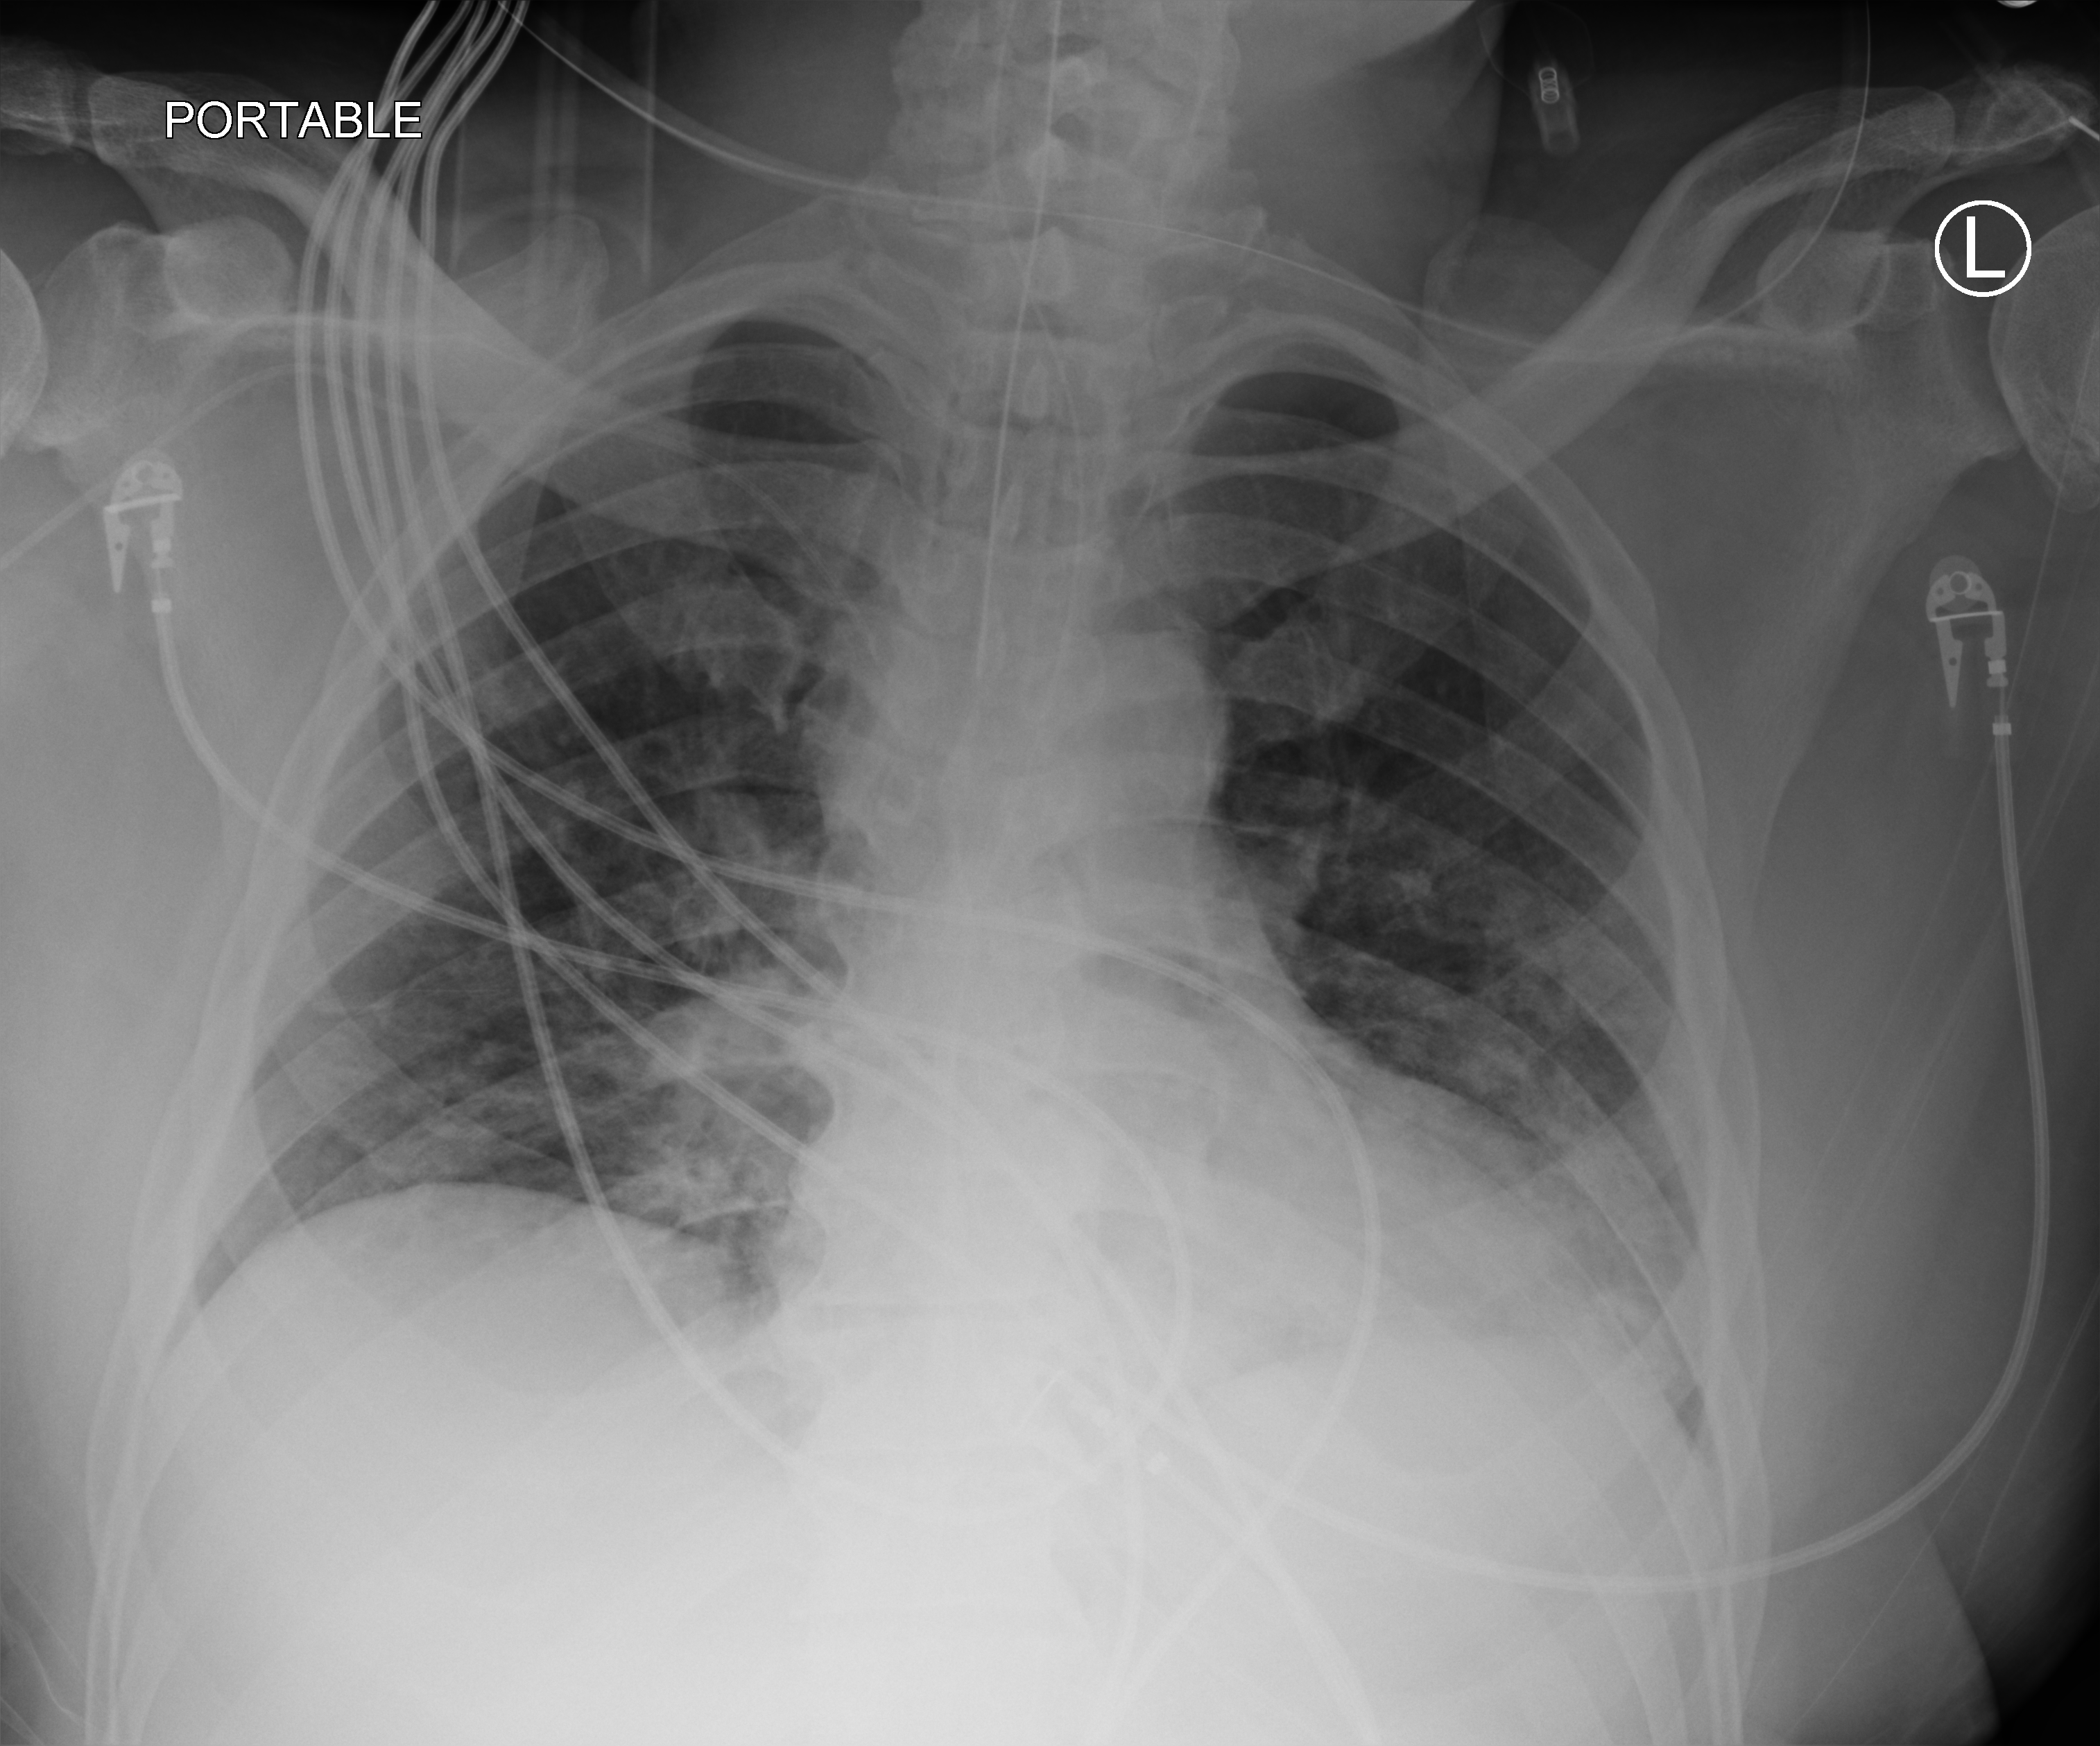
Chest X-ray (portable). Patient hospitalised with COVID-19; male, aged 18–59 years.
From the hospital-stay record, not from the radiograph (when in the stay this image was taken is not recorded): length of hospital stay: 41 days; diabetes (admission record): no; mechanically ventilated during this hospital stay: yes.